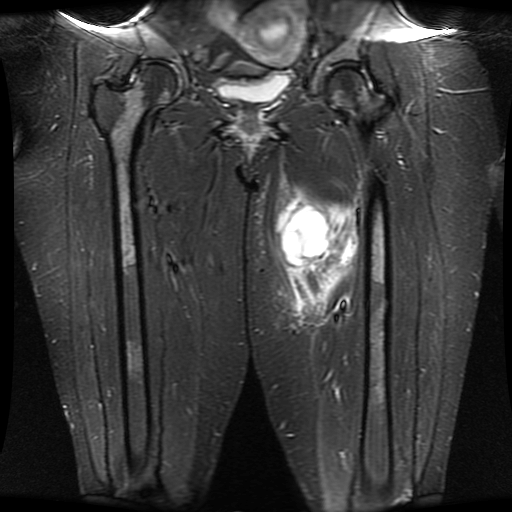
MRI of an extremity soft-tissue mass, one coronal slice. Slice 13 of 30 in the series (ordered by position). STIR. 512 × 512 image matrix, field of view 460 × 460 mm. Female patient. From the clinical record (not read from this slice): histological type: myxofibrosarcoma; grade: intermediate; site of the primary tumour: left thigh.
Annotated regions visible in this slice (manually delineated by an expert):
- gross tumour volume including surrounding oedema: box from (x=270, y=173) to (x=361, y=328) px
- gross tumour volume (mass): (x=278, y=202)–(x=336, y=268)